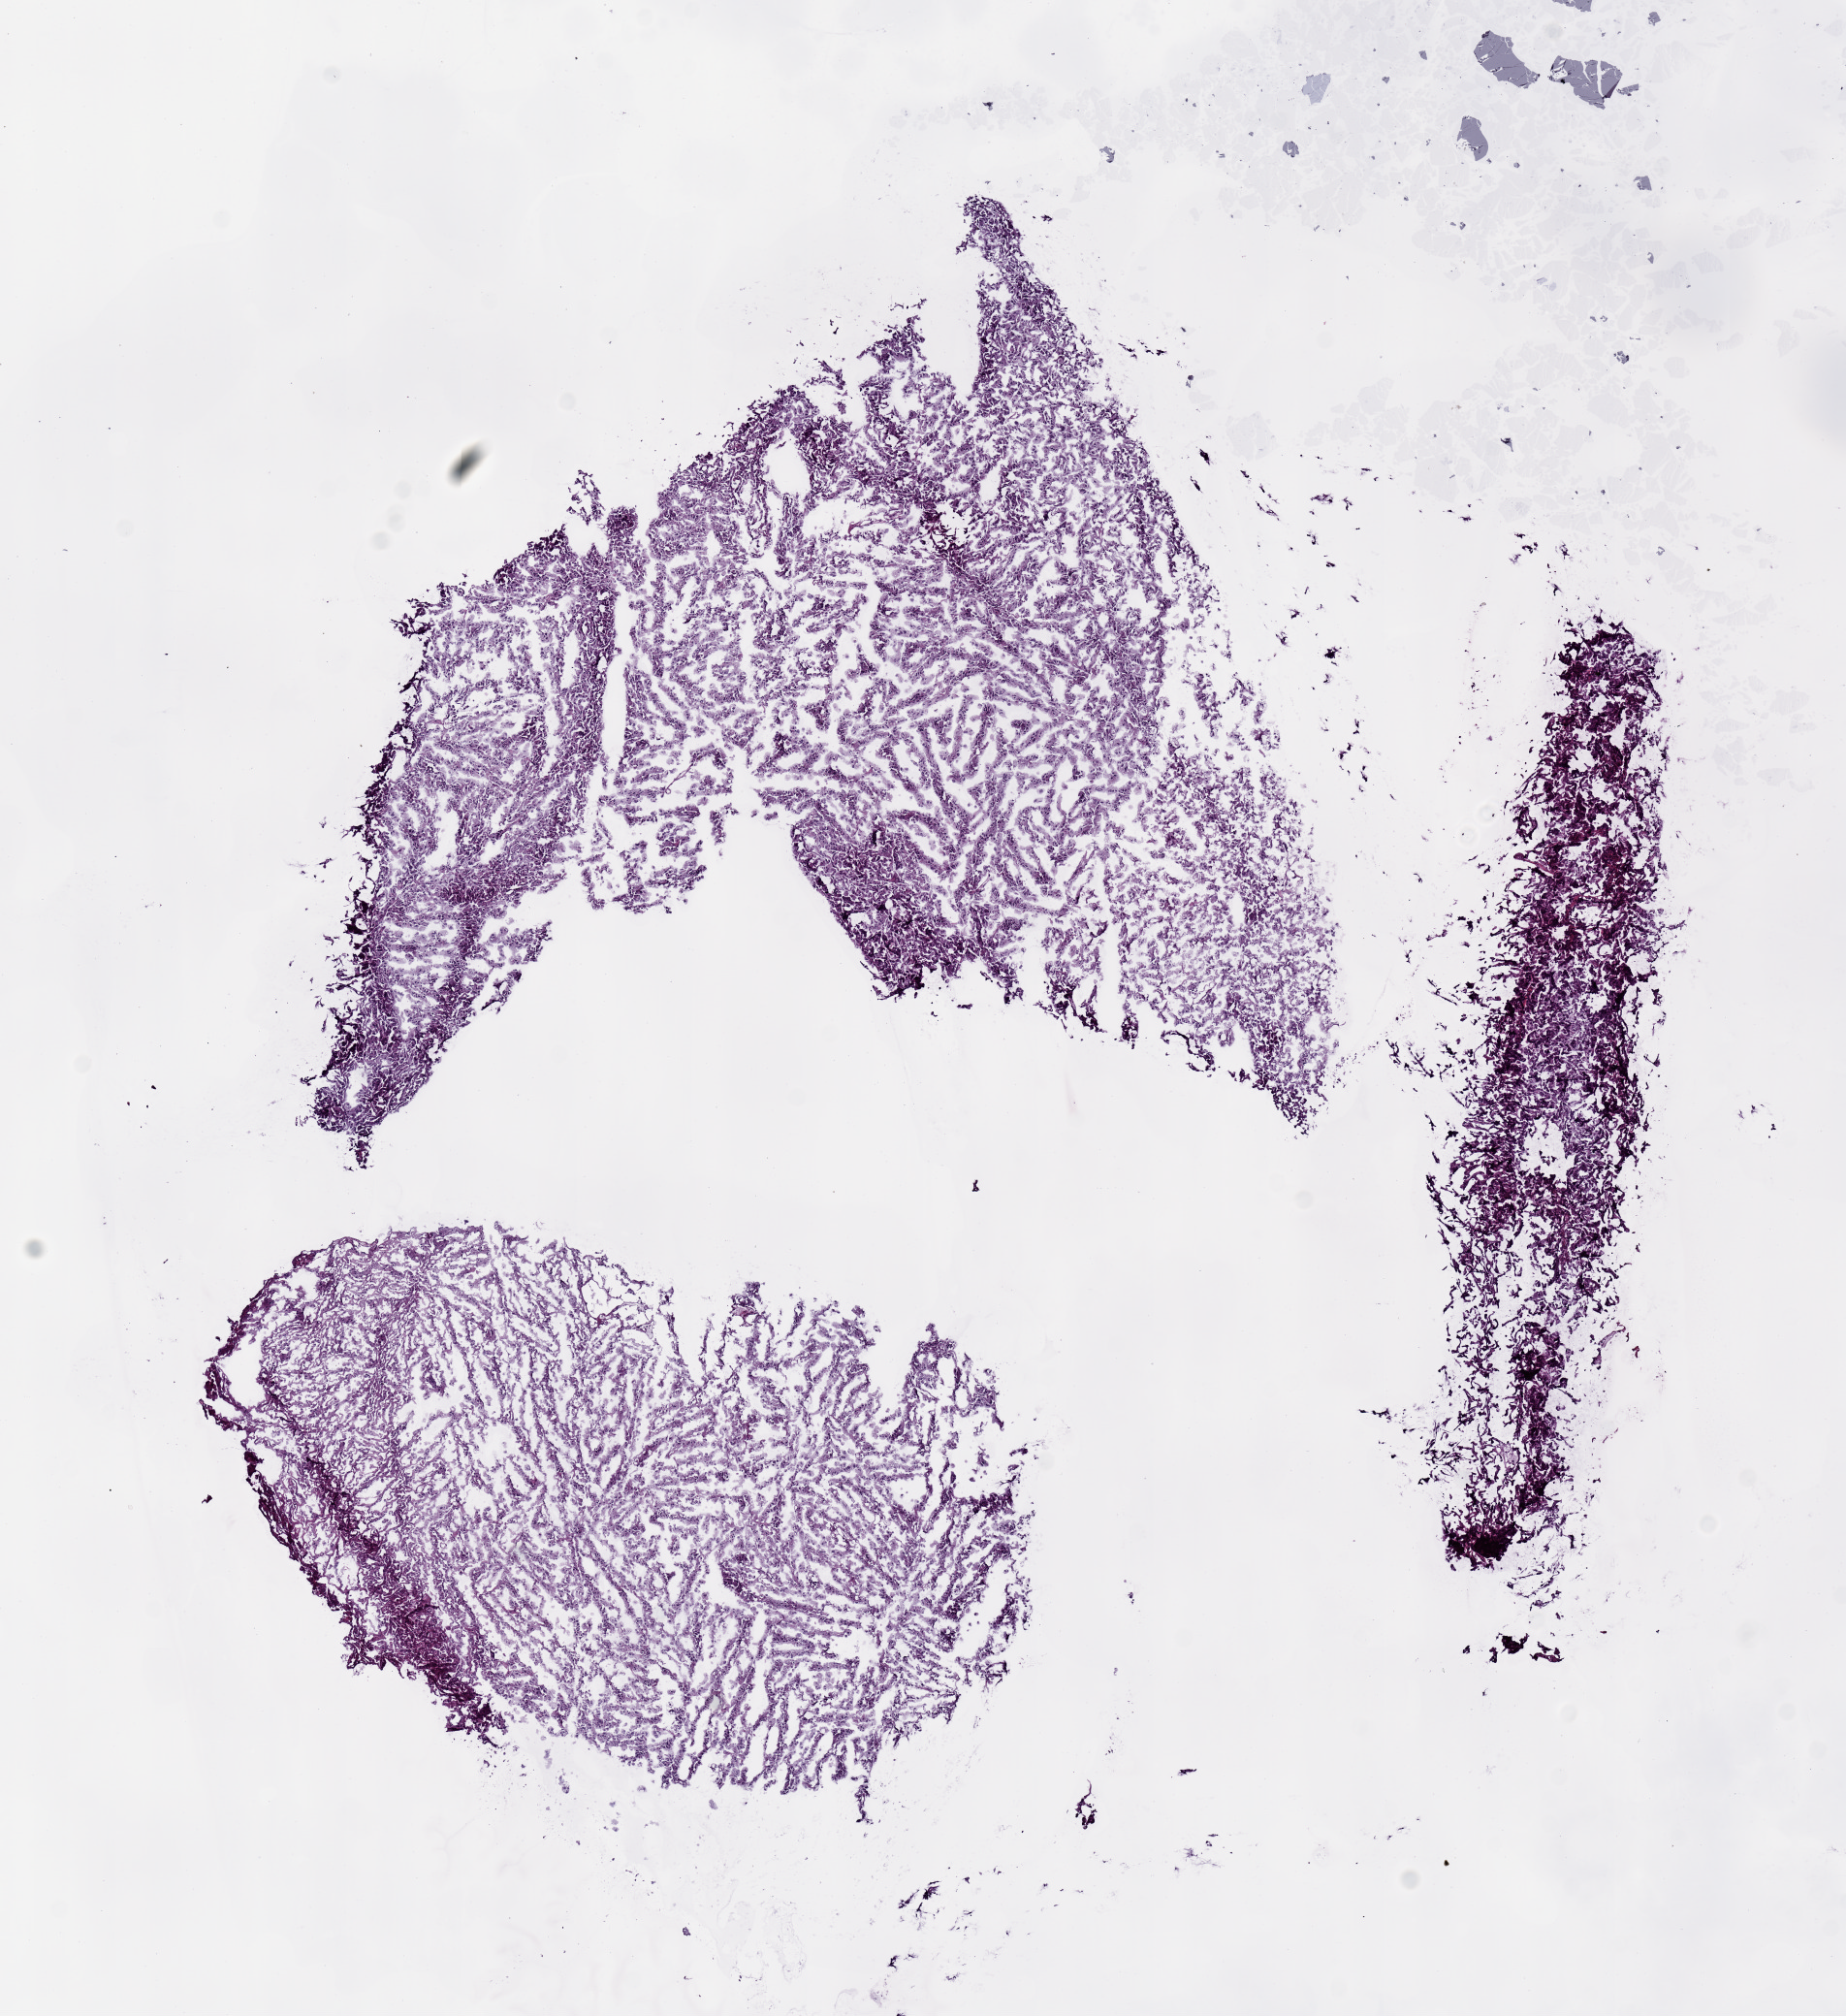
H&E whole-slide image — a low-resolution overview of the entire scanned area, about 7.6 x 8.3 mm (from a 20x scan). Frozen section from the top of the tissue portion. Brain, primary tumour sample. Male patient; age at initial diagnosis 40 years. Histologic grade: G3 (poorly differentiated). Composition of this section per pathologist review: tumour cells 100%, tumour nuclei 80%, normal cells 0%, stromal cells 0%, necrosis 0%.
Histologic diagnosis: Astrocytoma, anaplastic.